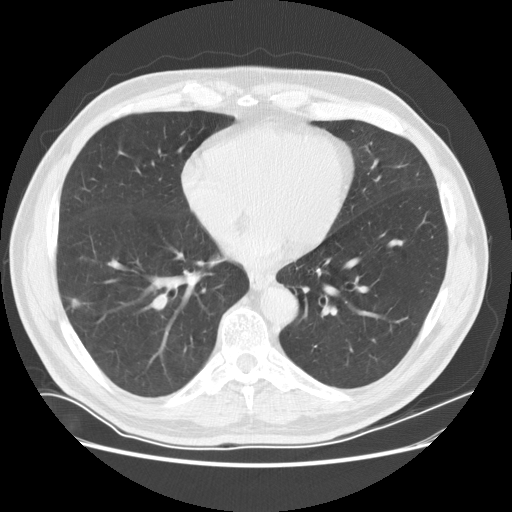
Low-dose screening chest CT, one axial slice; position 72 of 169 along the scan axis; reconstruction kernel STANDARD; 120 kVp; lung window (W 1500 / L -600 HU); 512 × 512 image matrix, field of view 380 × 380 mm.
Annotated regions visible in this slice (outlined manually by an expert reader):
- lesion 1 (tumor, lower lobe of right lung): bounding box (x1, y1, x2, y2) in pixels: (72, 299, 81, 308)